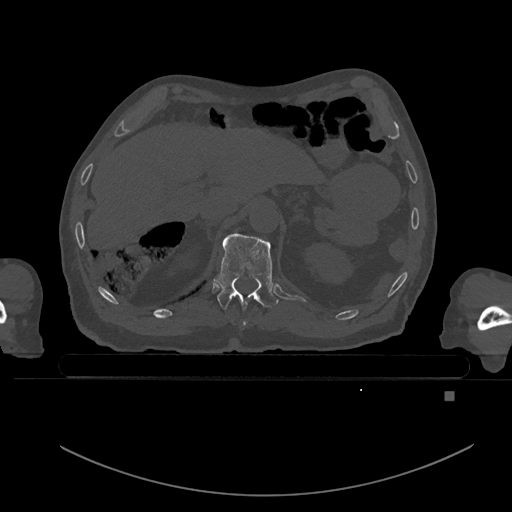
CT including the spine, one axial slice; slice 35 of 969 in the series (ordered by position); bone window (W 1800 / L 400 HU); 0.5 mm slice thickness; 512 × 512 image matrix, field of view 456 × 456 mm. Male patient, age 82 years. From the clinical record (not read from this slice): primary cancer: prostate.
Structures marked on this image (semi-automatically segmented with operator editing):
- T11 vertebra: bounding box [x1, y1, x2, y2] px = [214, 233, 278, 325]